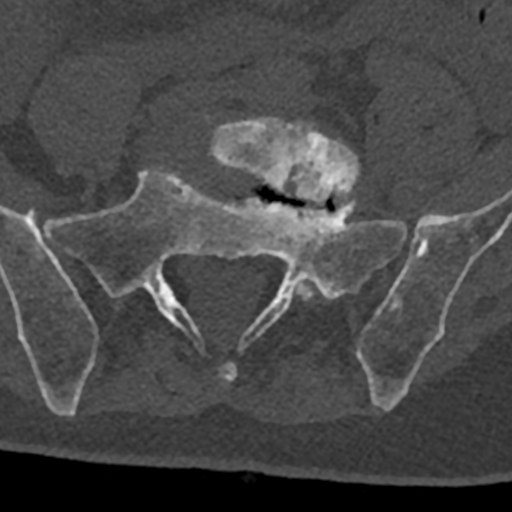
CT including the spine, one axial slice; position 160 of 797 along the scan axis; 120 kVp; bone window (W 1800 / L 400 HU); 0.5 mm slice thickness; 512 × 512 image matrix. Male patient, age 74 years. From the clinical record (not read from this slice): primary cancer: renal; vertebrae with lytic lesions (as recorded): T10, L1, L2, L3, L4, L5.
Outlined on this slice (semi-automatically segmented with operator editing):
- L5 vertebra: box from (x=207, y=118) to (x=360, y=301) px